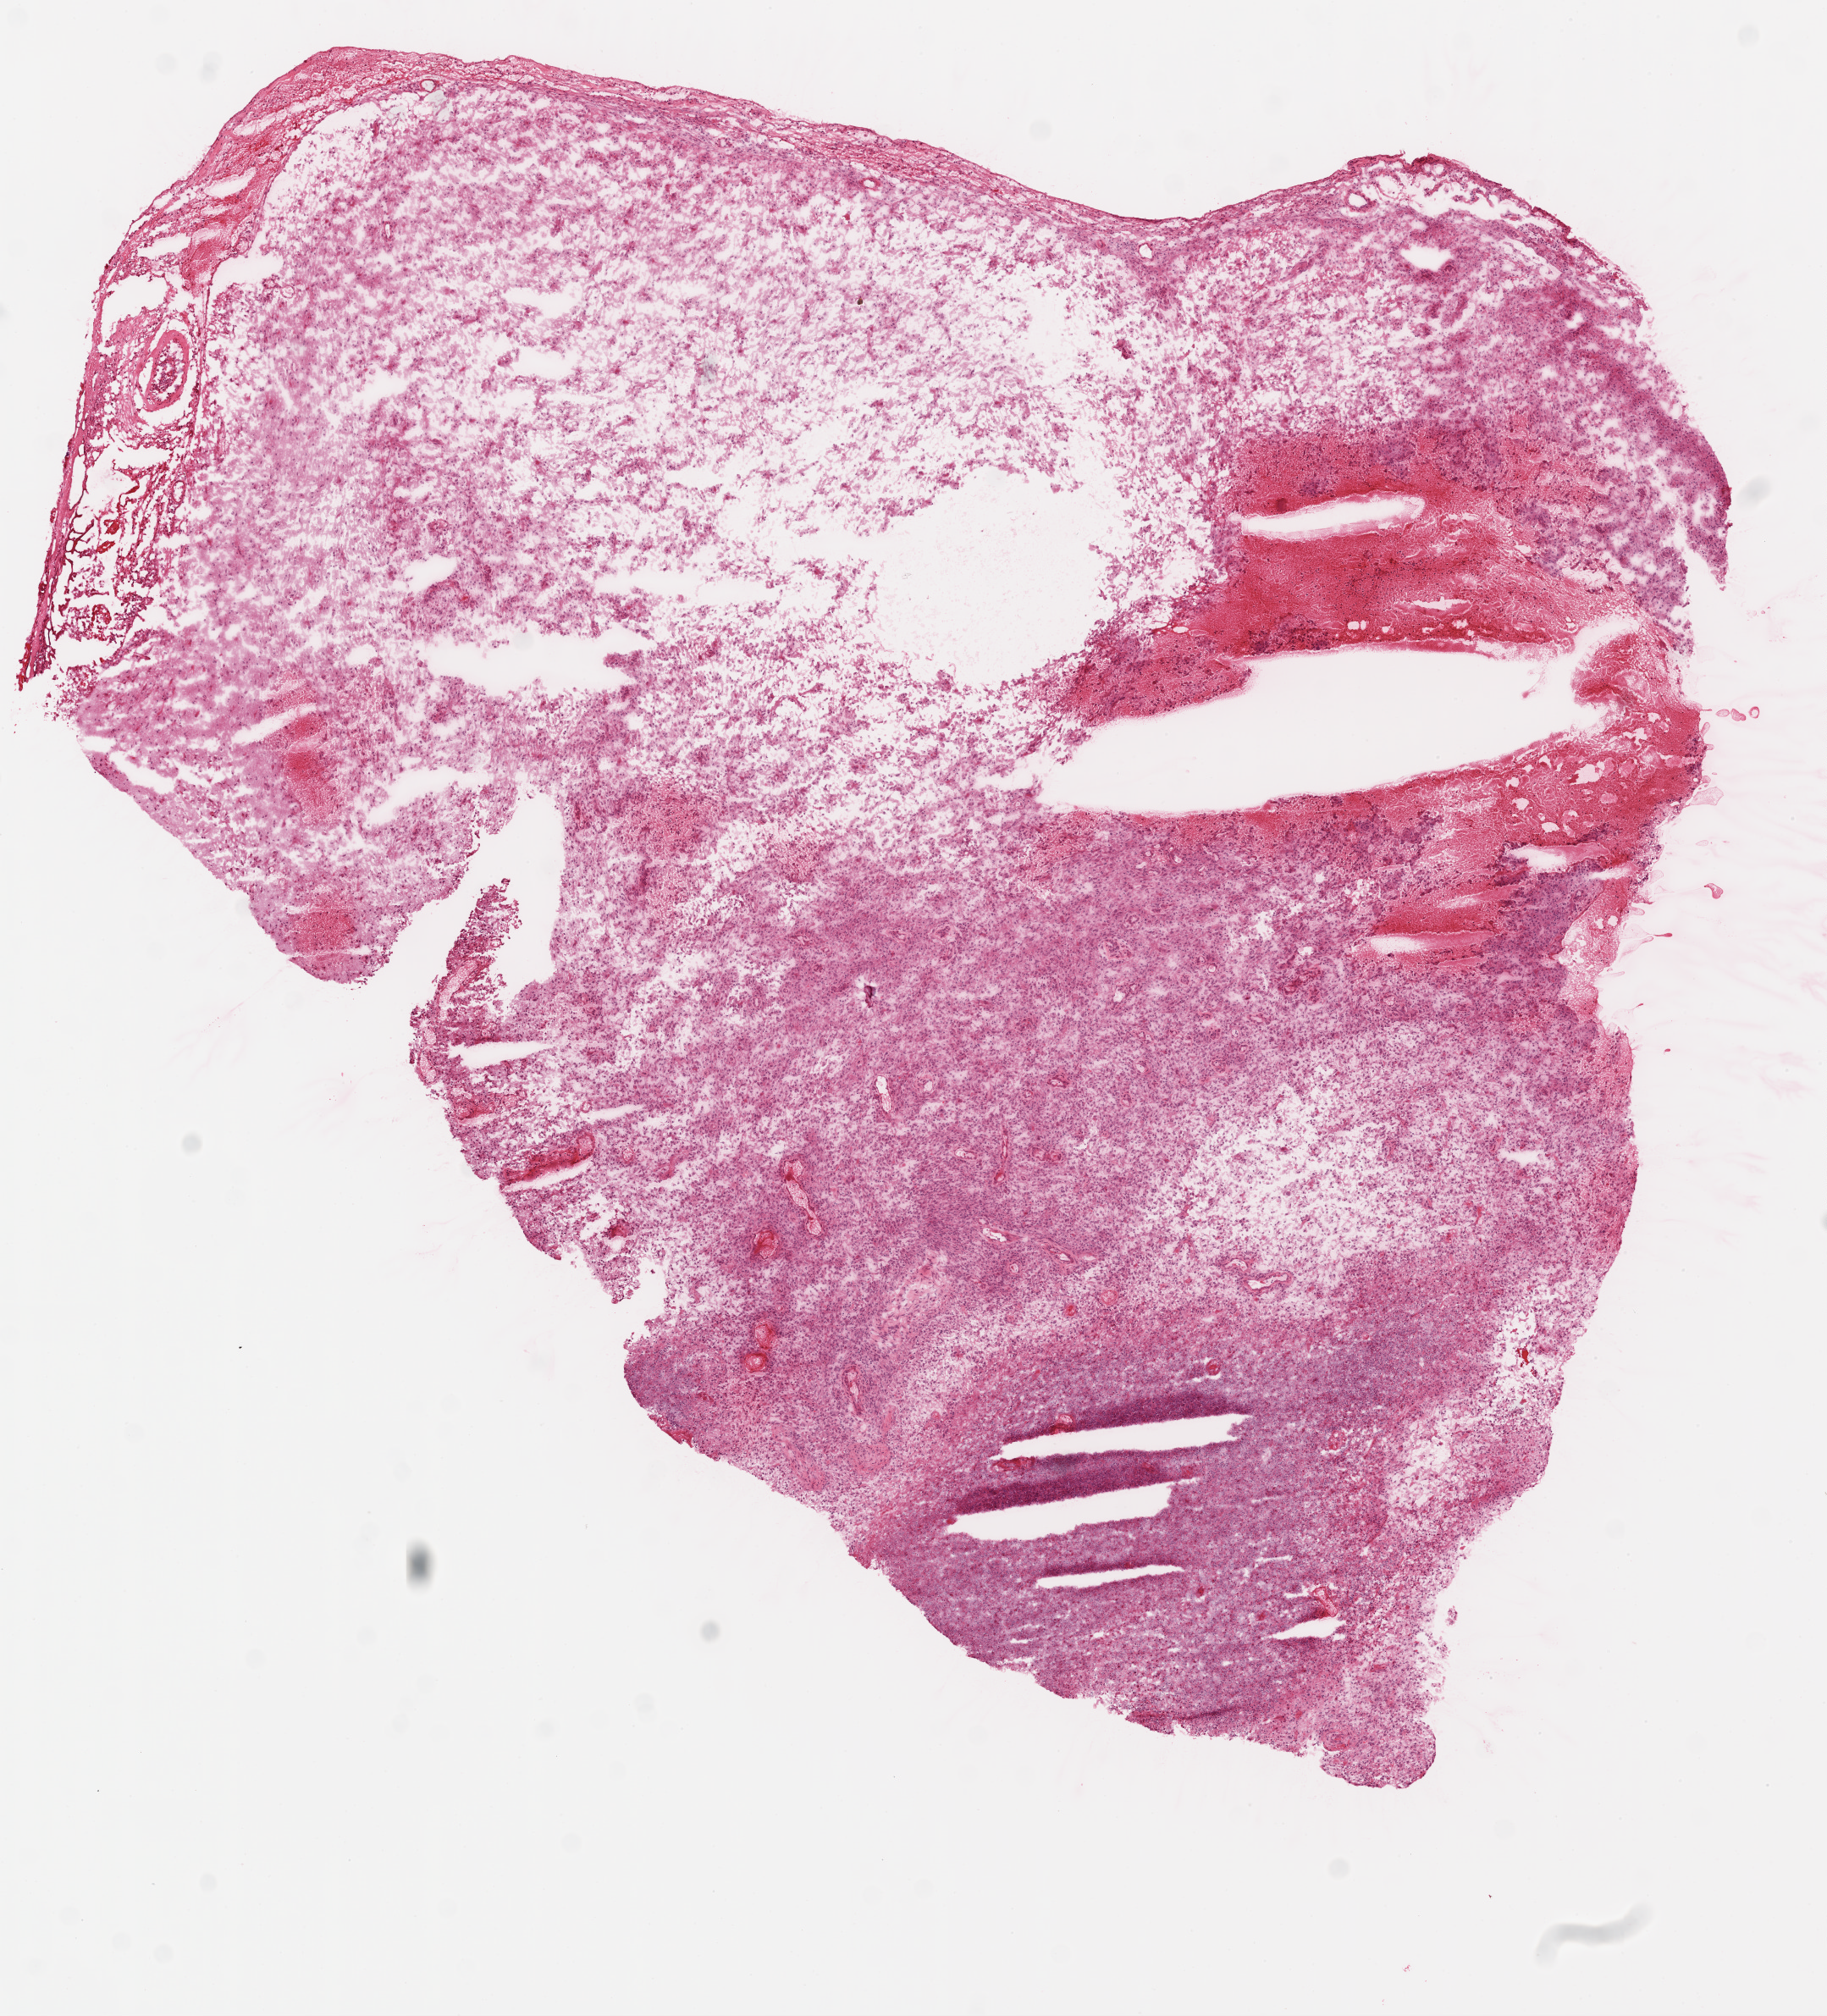
Digitized H&E-stained tissue section (whole slide) — whole scanned area (about 8.7 x 9.6 mm, from a 20x scan) shown as a low-resolution overview. Frozen section from the top of the tissue portion. Primary tumour sample from the brain. Female patient; age at initial diagnosis 75 years. Pathologist review of this section (percent, as recorded): tumour cells 35%, tumour nuclei 80%, normal cells 0%, stromal cells 40%, necrosis 25%.
- pathologic diagnosis: Glioblastoma